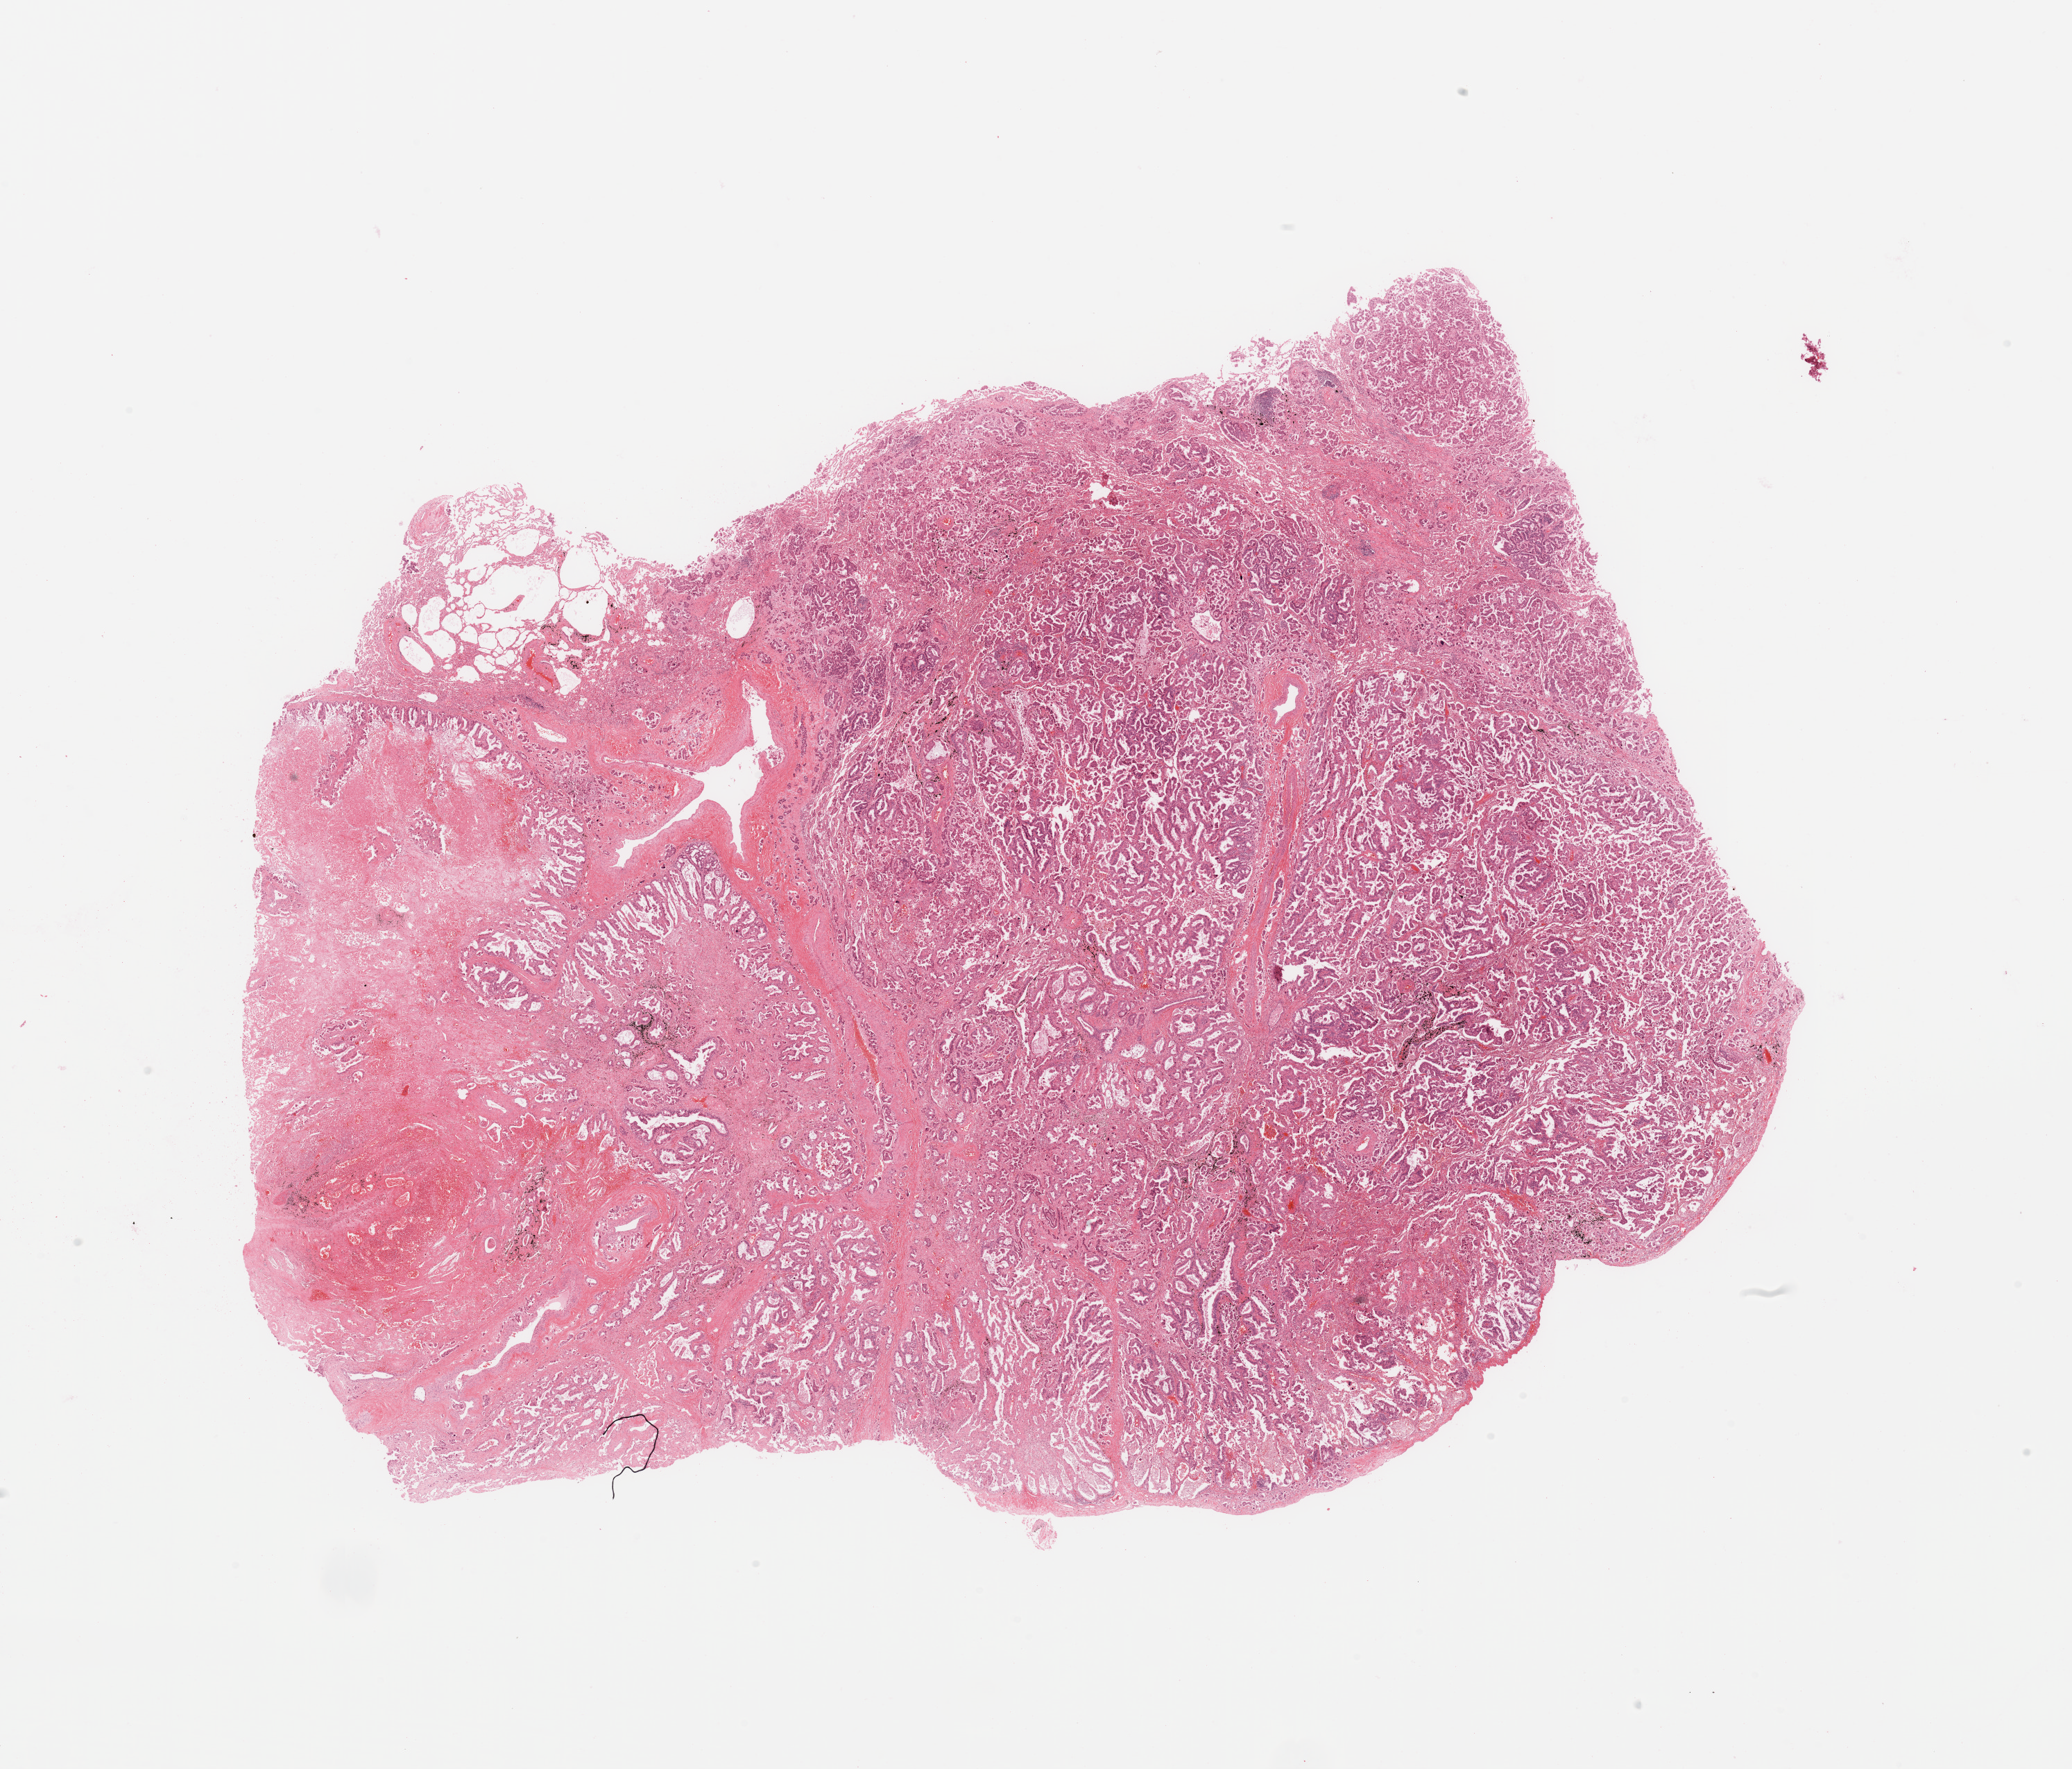
Digitized Hematoxylin and eosin (H&E) stained tissue section (whole slide), low-resolution overview of the scanned area, about 23.6 x 20.2 mm (slide scanned at 20x), lung, tumour tissue. Patient: male, age 64 years. Histologic grade: G2 (moderately differentiated).
- AJCC pathologic stage: IIA
- diagnosis: Adenocarcinoma, NOS